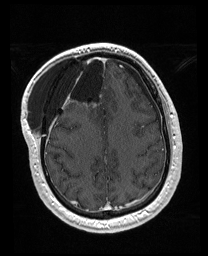
Brain MRI from a brain-tumour surgery series, one axial slice. Position 60 of 176 along the scan axis. T1-weighted post-contrast. 1 mm slice thickness. 208 × 256 image matrix, field of view 208 × 256 mm. From the clinical record (not read from this slice): histopathology: Astrocytoma; WHO grade: 4; IDH mutation: yes; tumour location: Right Orbitofrontal Anterior Temporal Insular.
Outlined on this slice (expert manual segmentation):
- previous resection cavity: bounding box (x1, y1, x2, y2) in pixels: (56, 54, 106, 100)